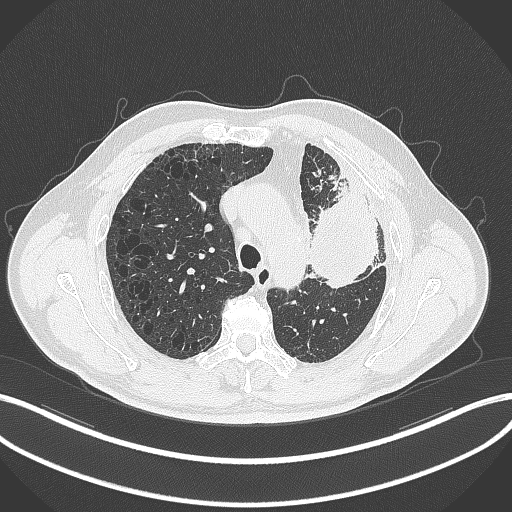
Chest CT, one axial slice. Slice 228 of 297 in the series (ordered by position). Lung window (W 1500 / L -600 HU). 1 mm slice thickness. 512 × 512 image matrix. Male patient, age 68 years. From the clinical record (not read from this slice): clinical TNM (as recorded): T3 N3 M1.
Structures marked on this image (bounding box drawn by a radiologist):
- lung tumour (recorded histology: adenocarcinoma): box from (x=301, y=180) to (x=385, y=295) px